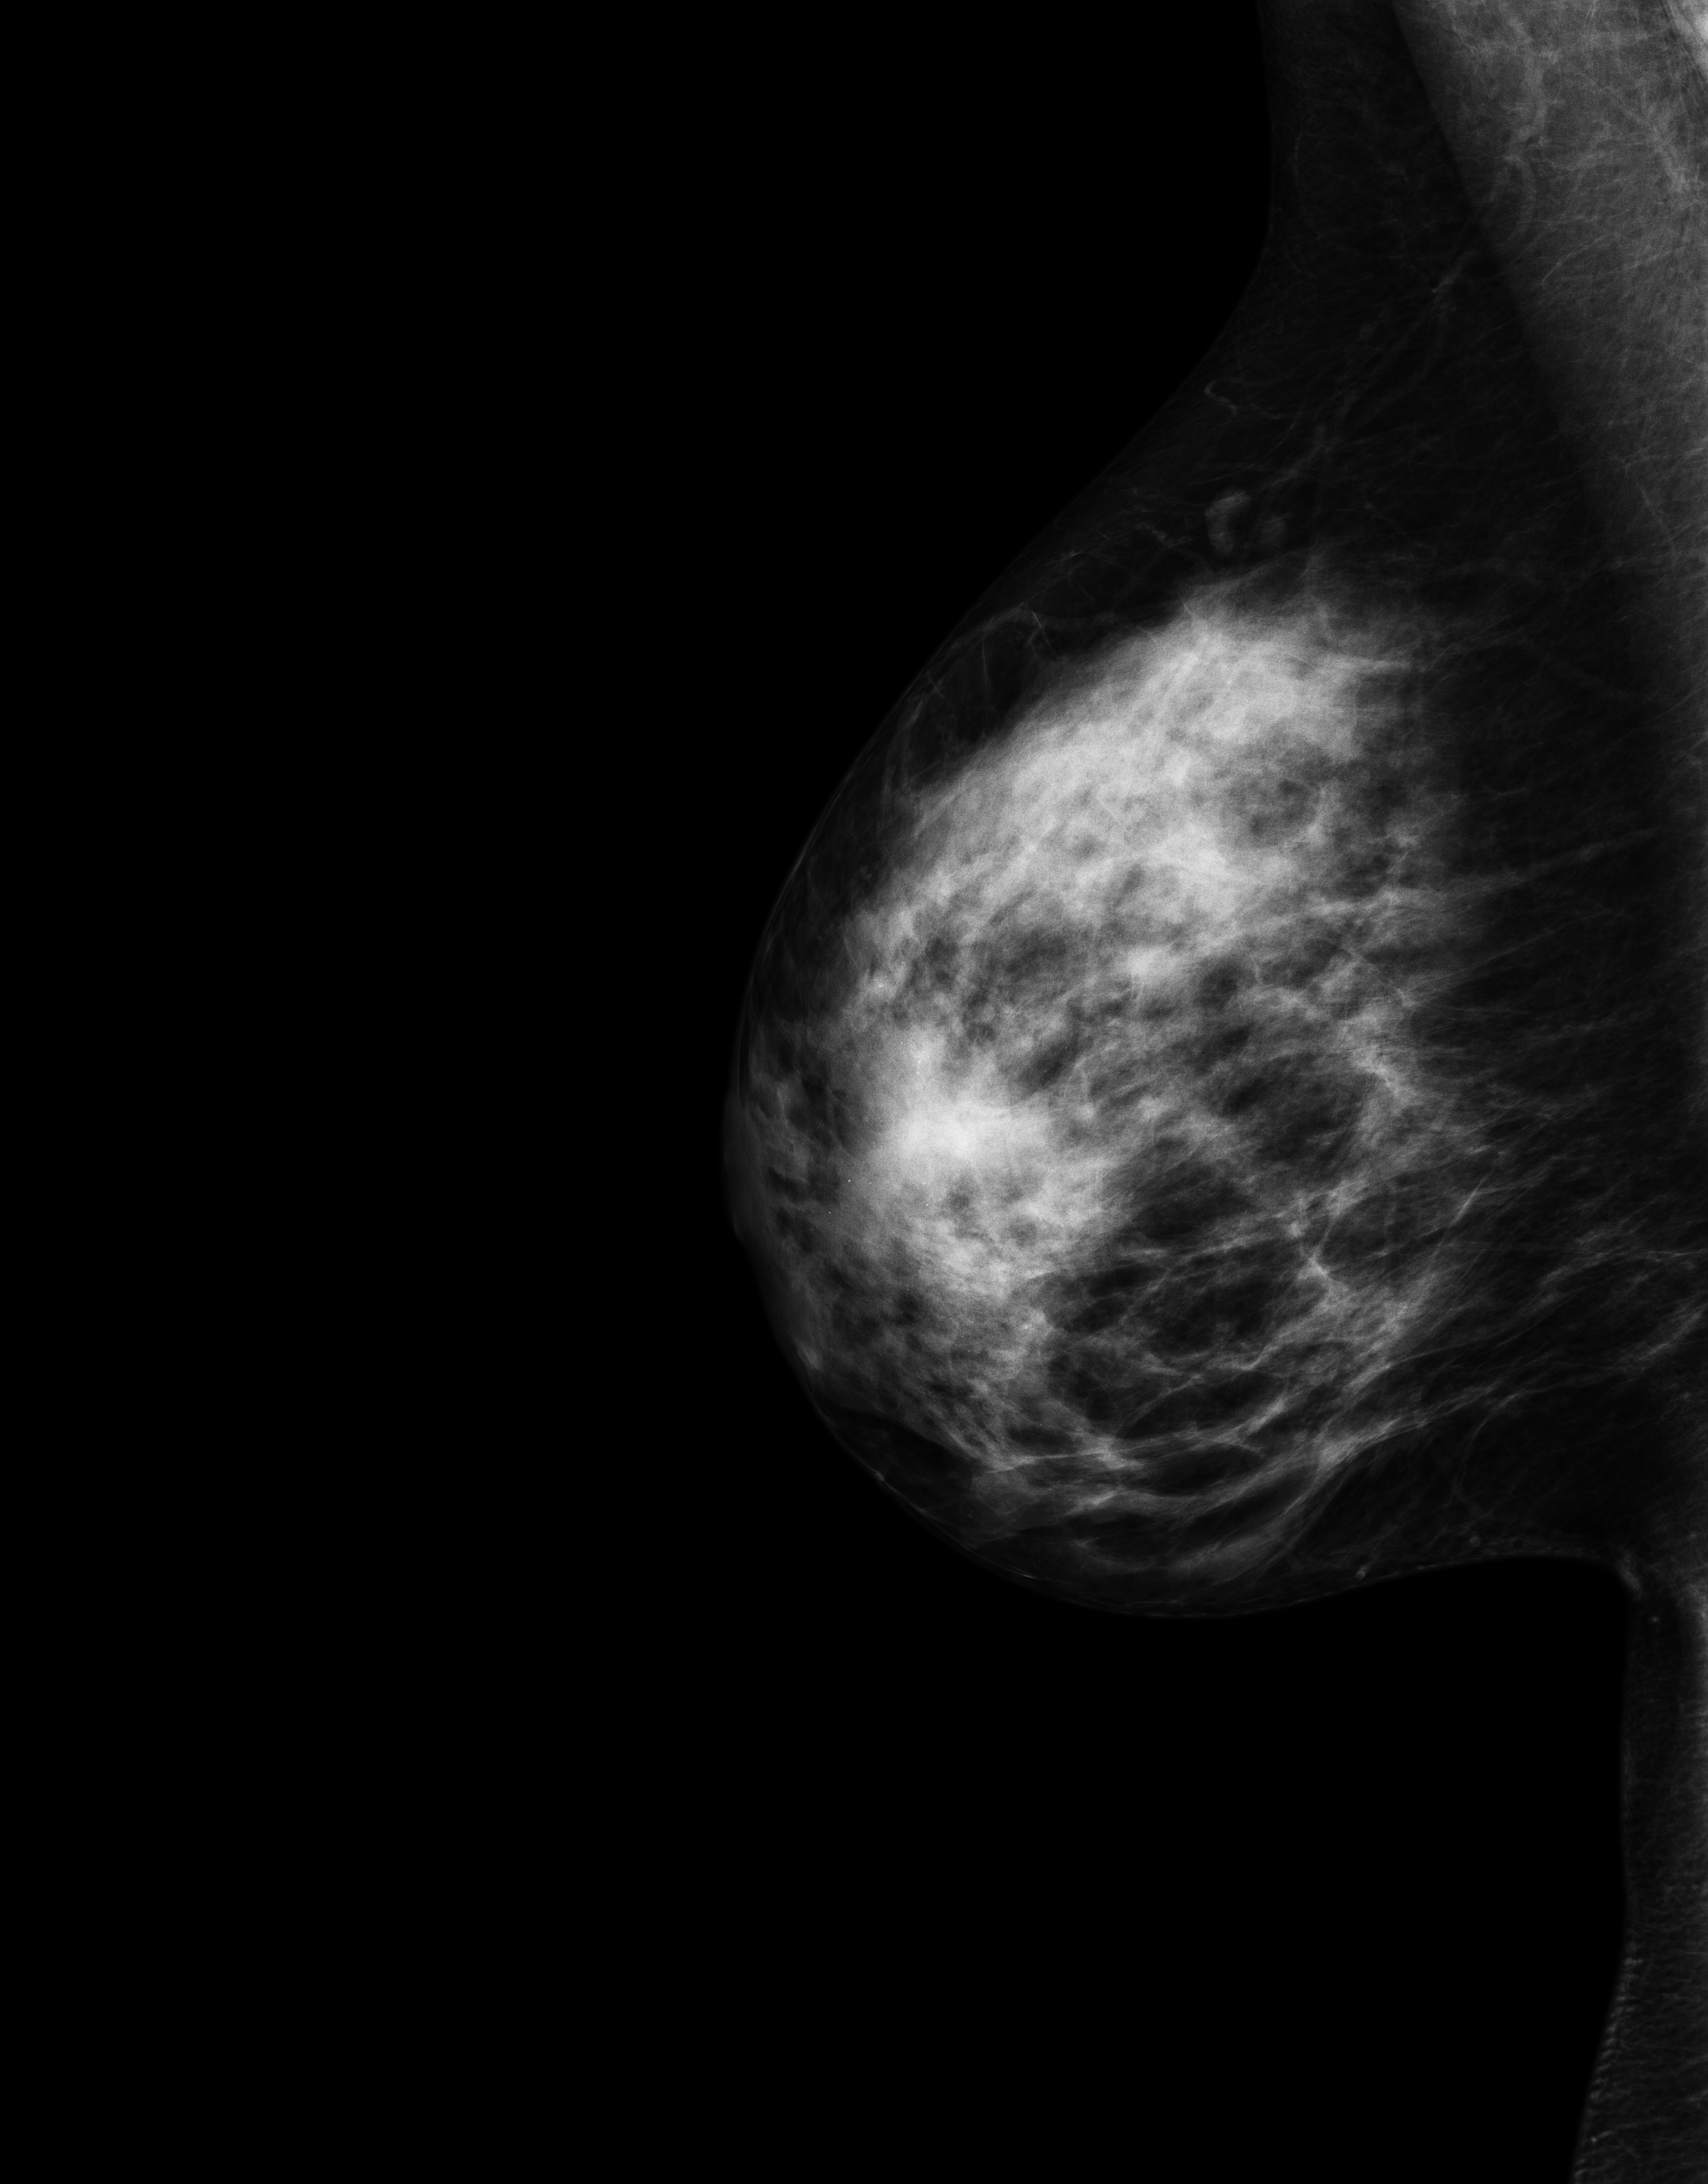
Digital mammogram (FFDM), right breast, medio-lateral oblique projection, annual screening mammography examination, compressed breast thickness 63 mm, system: Senographe Essential ADS_56.21.3. Patient: female, 46 years.
BI-RADS breast density category at the screening exam (both breasts, scale 1–4): 3. Final BI-RADS assessment for this screening round (tomosynthesis exam, both breasts): category 1. Recall: no recall after this screen.